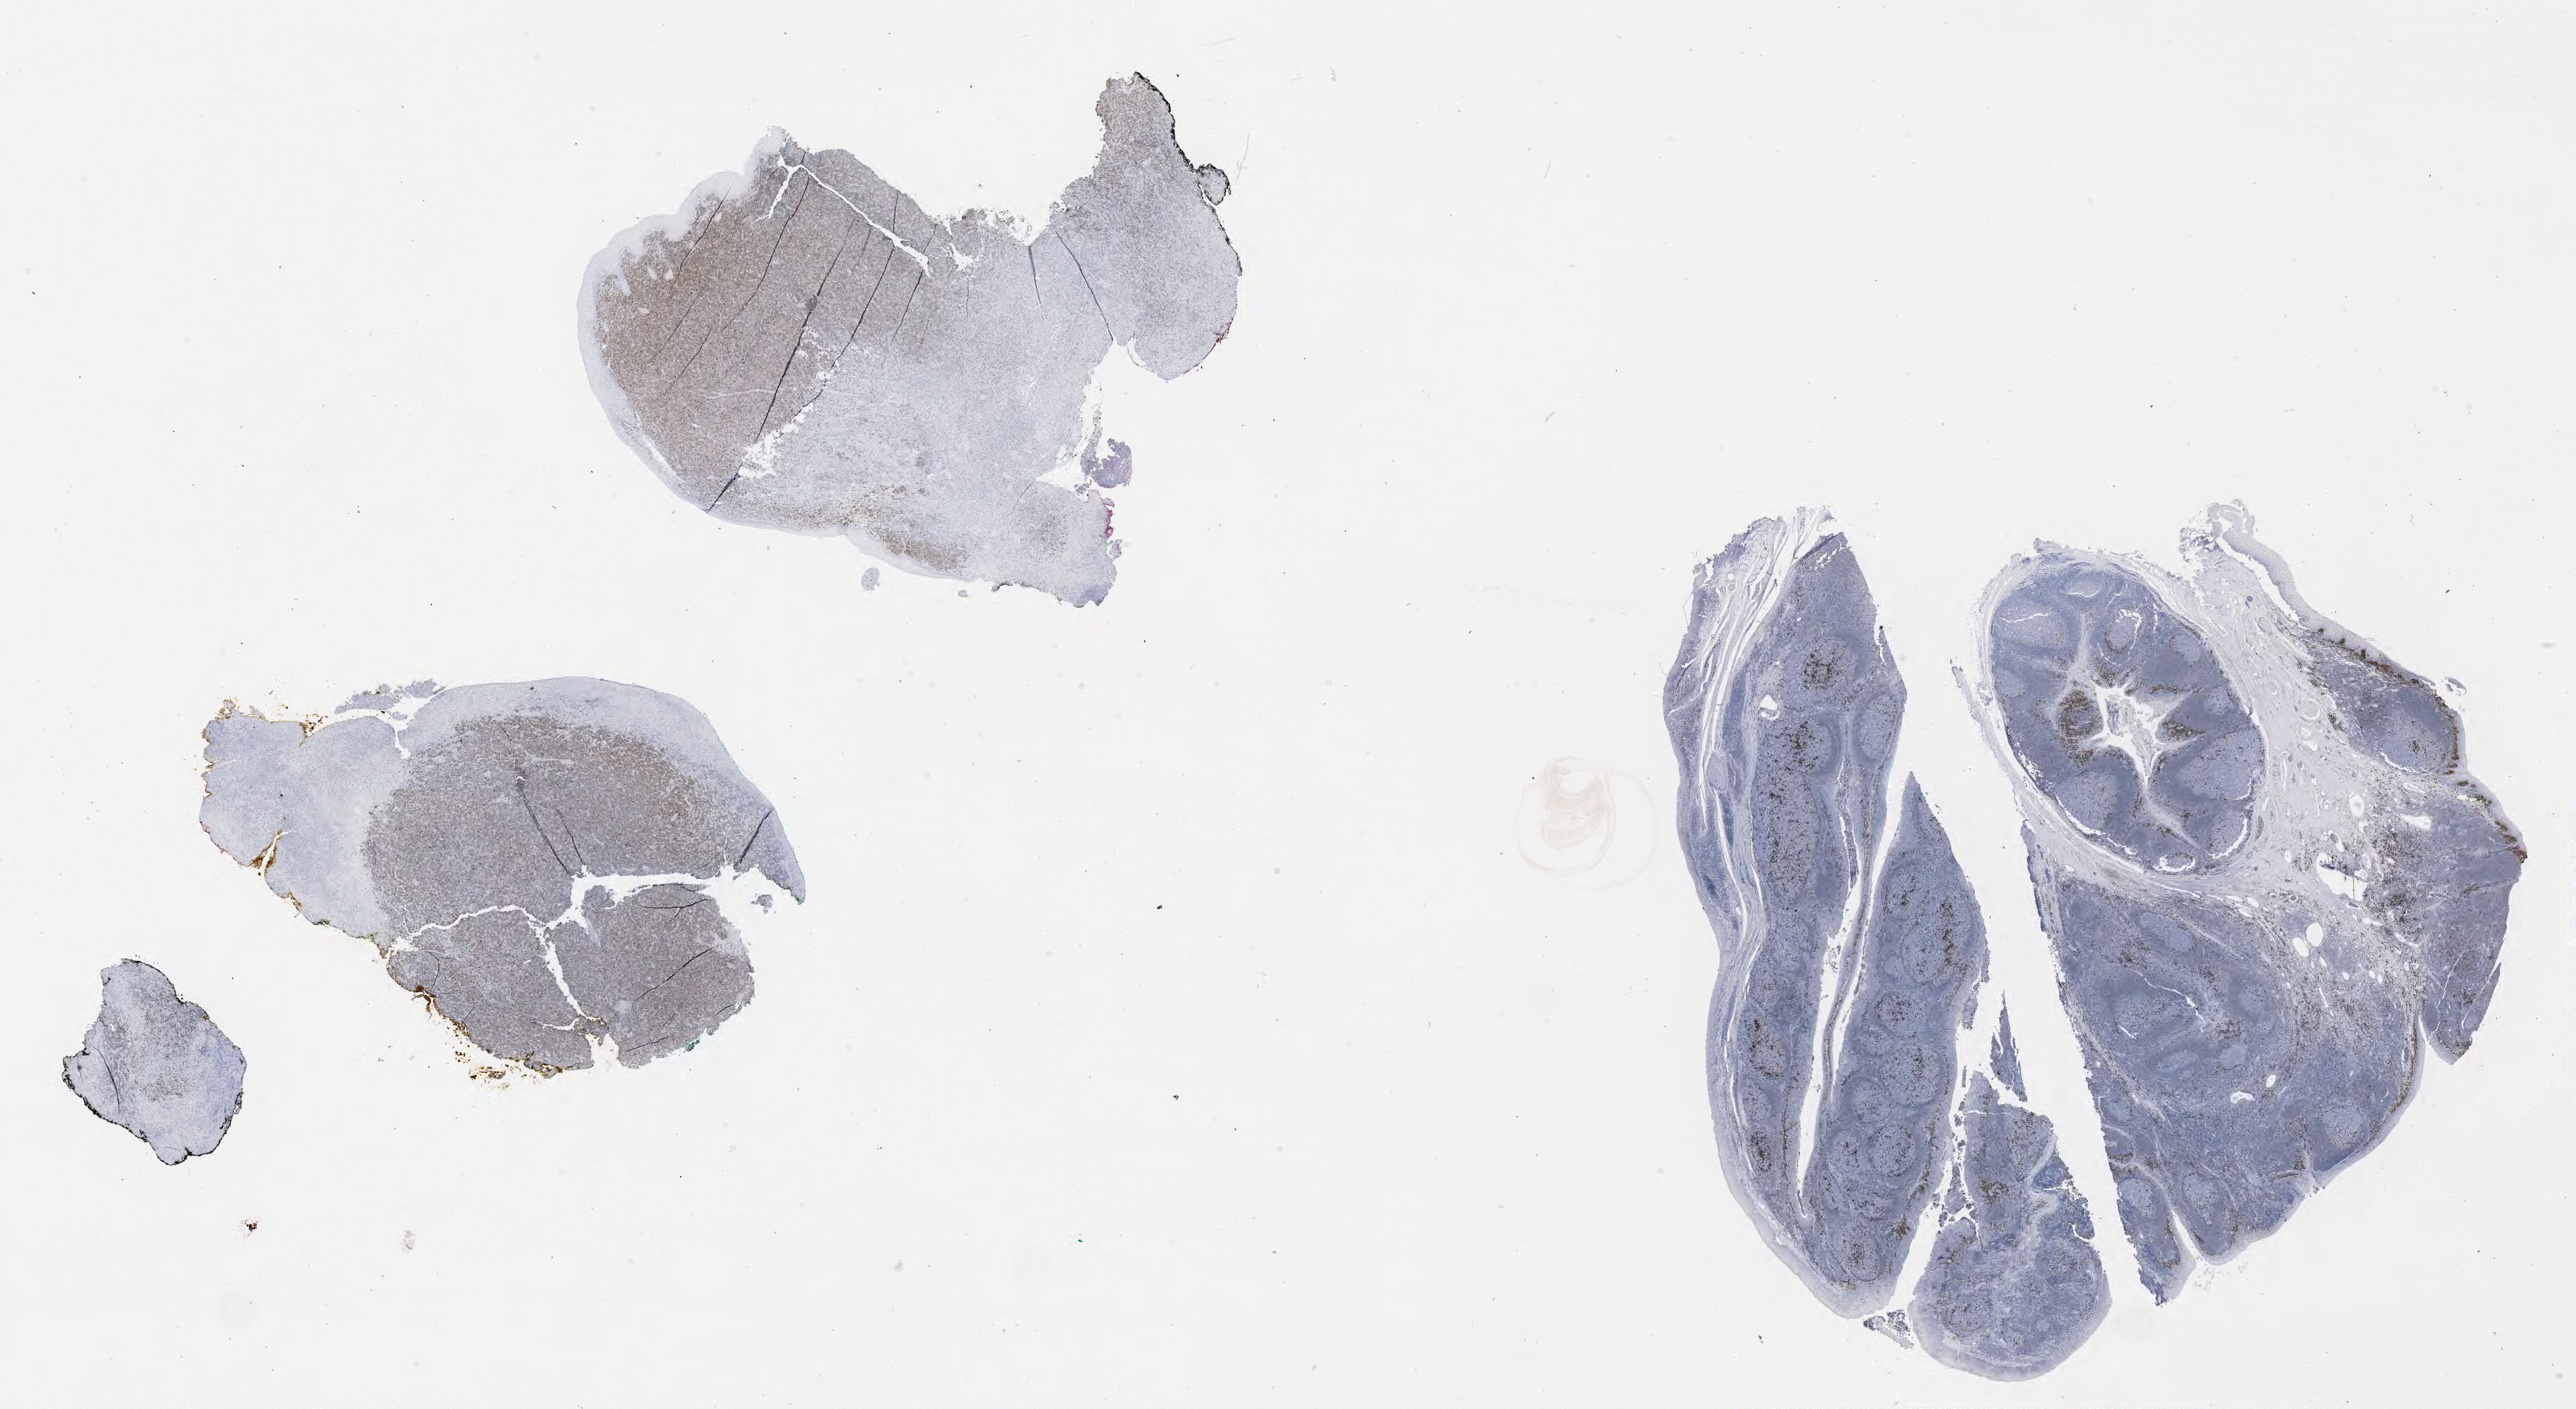
Whole-slide image, immunohistochemical stain for IRF4/MUM1, a low-resolution overview of the entire scanned area, about 31.7 x 17.3 mm; specimen: tumor tissue. Male patient, 49 years old.
Histologic diagnosis: Diffuse large B-cell lymphoma, NOS.